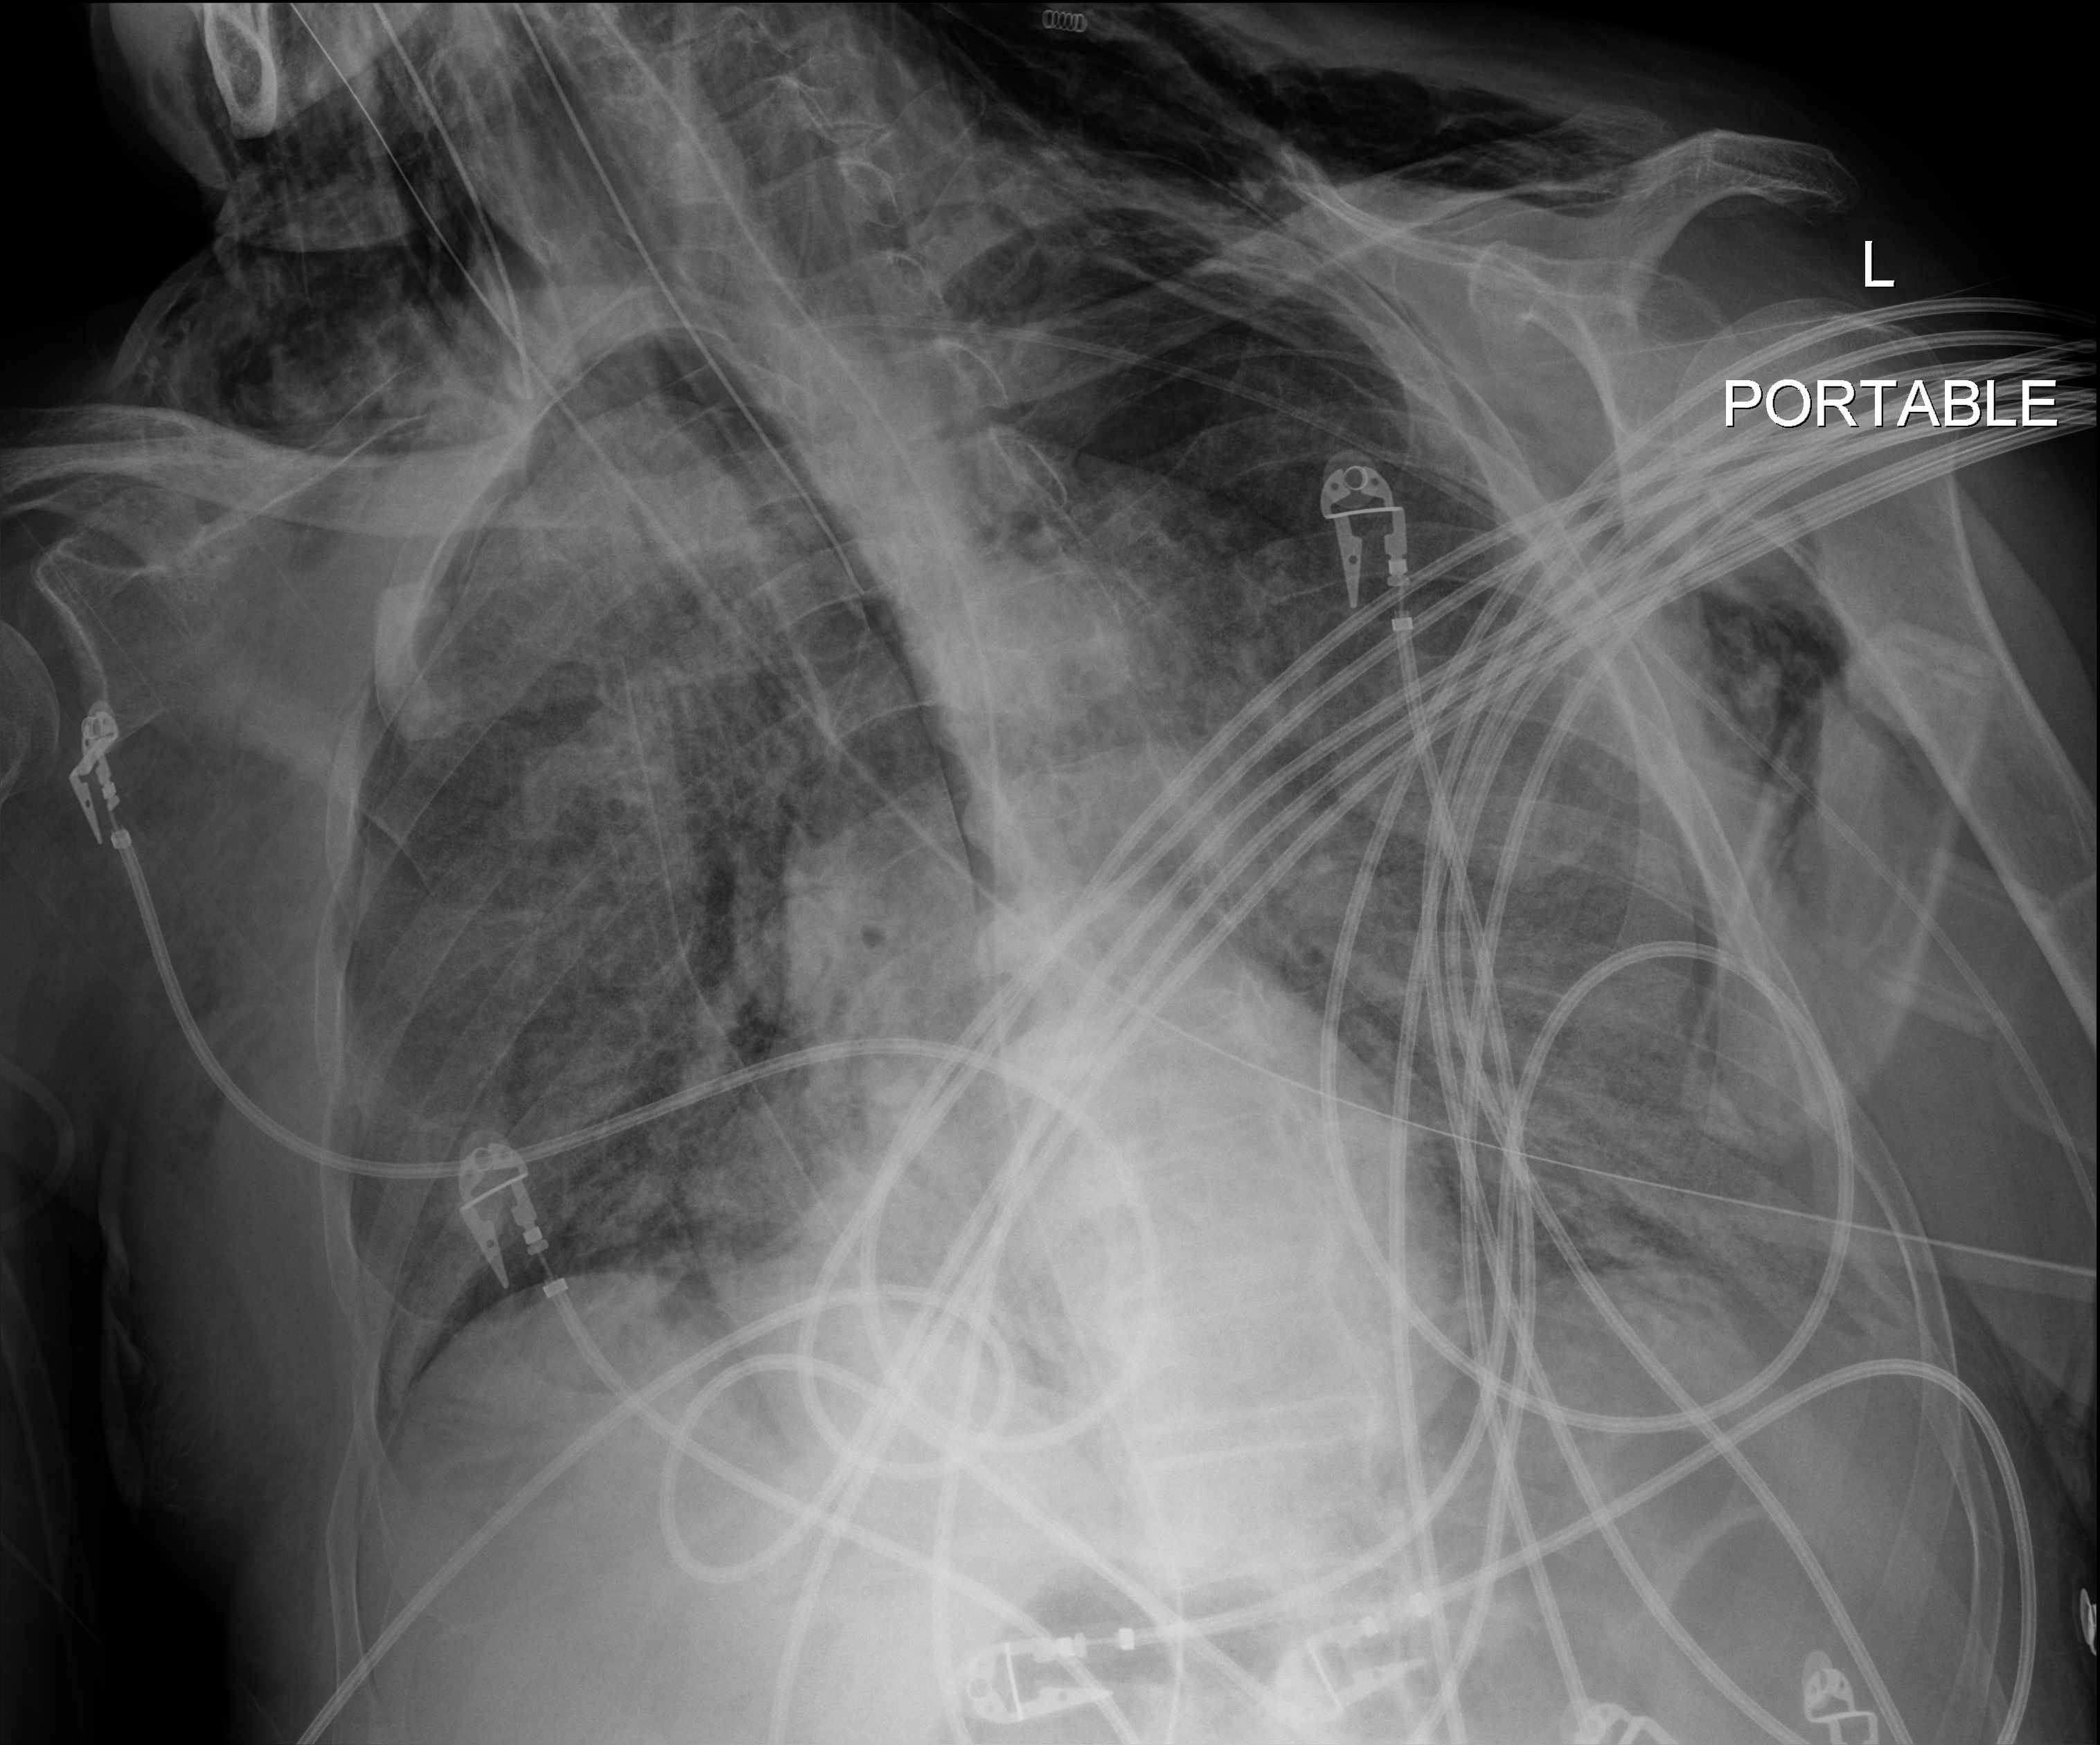
Chest X-ray (portable); anteroposterior (AP) projection. Patient hospitalised with COVID-19; male, aged 75–90 years.
Admission-level facts for this patient (not findings on this image; timing relative to this image not recorded):
- length of hospital stay: 30 days